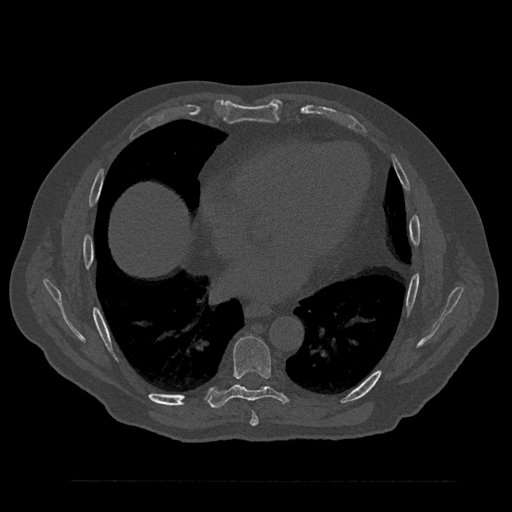
CT including the spine, one axial slice; slice 457 of 797 in the series (ordered by position); reconstruction kernel Br40s/3; 120 kVp; bone window (W 1800 / L 400 HU); 0.5 mm slice thickness; 512 × 512 image matrix, field of view 430 × 430 mm. Male patient, age 61 years. From the clinical record (not read from this slice): primary cancer: prostate.
Structures marked on this image (semi-automatic segmentation, software-assisted and operator-edited):
- T7 vertebra: box from (x=250, y=412) to (x=259, y=426) px
- T8 vertebra: (x=209, y=336)–(x=289, y=409)